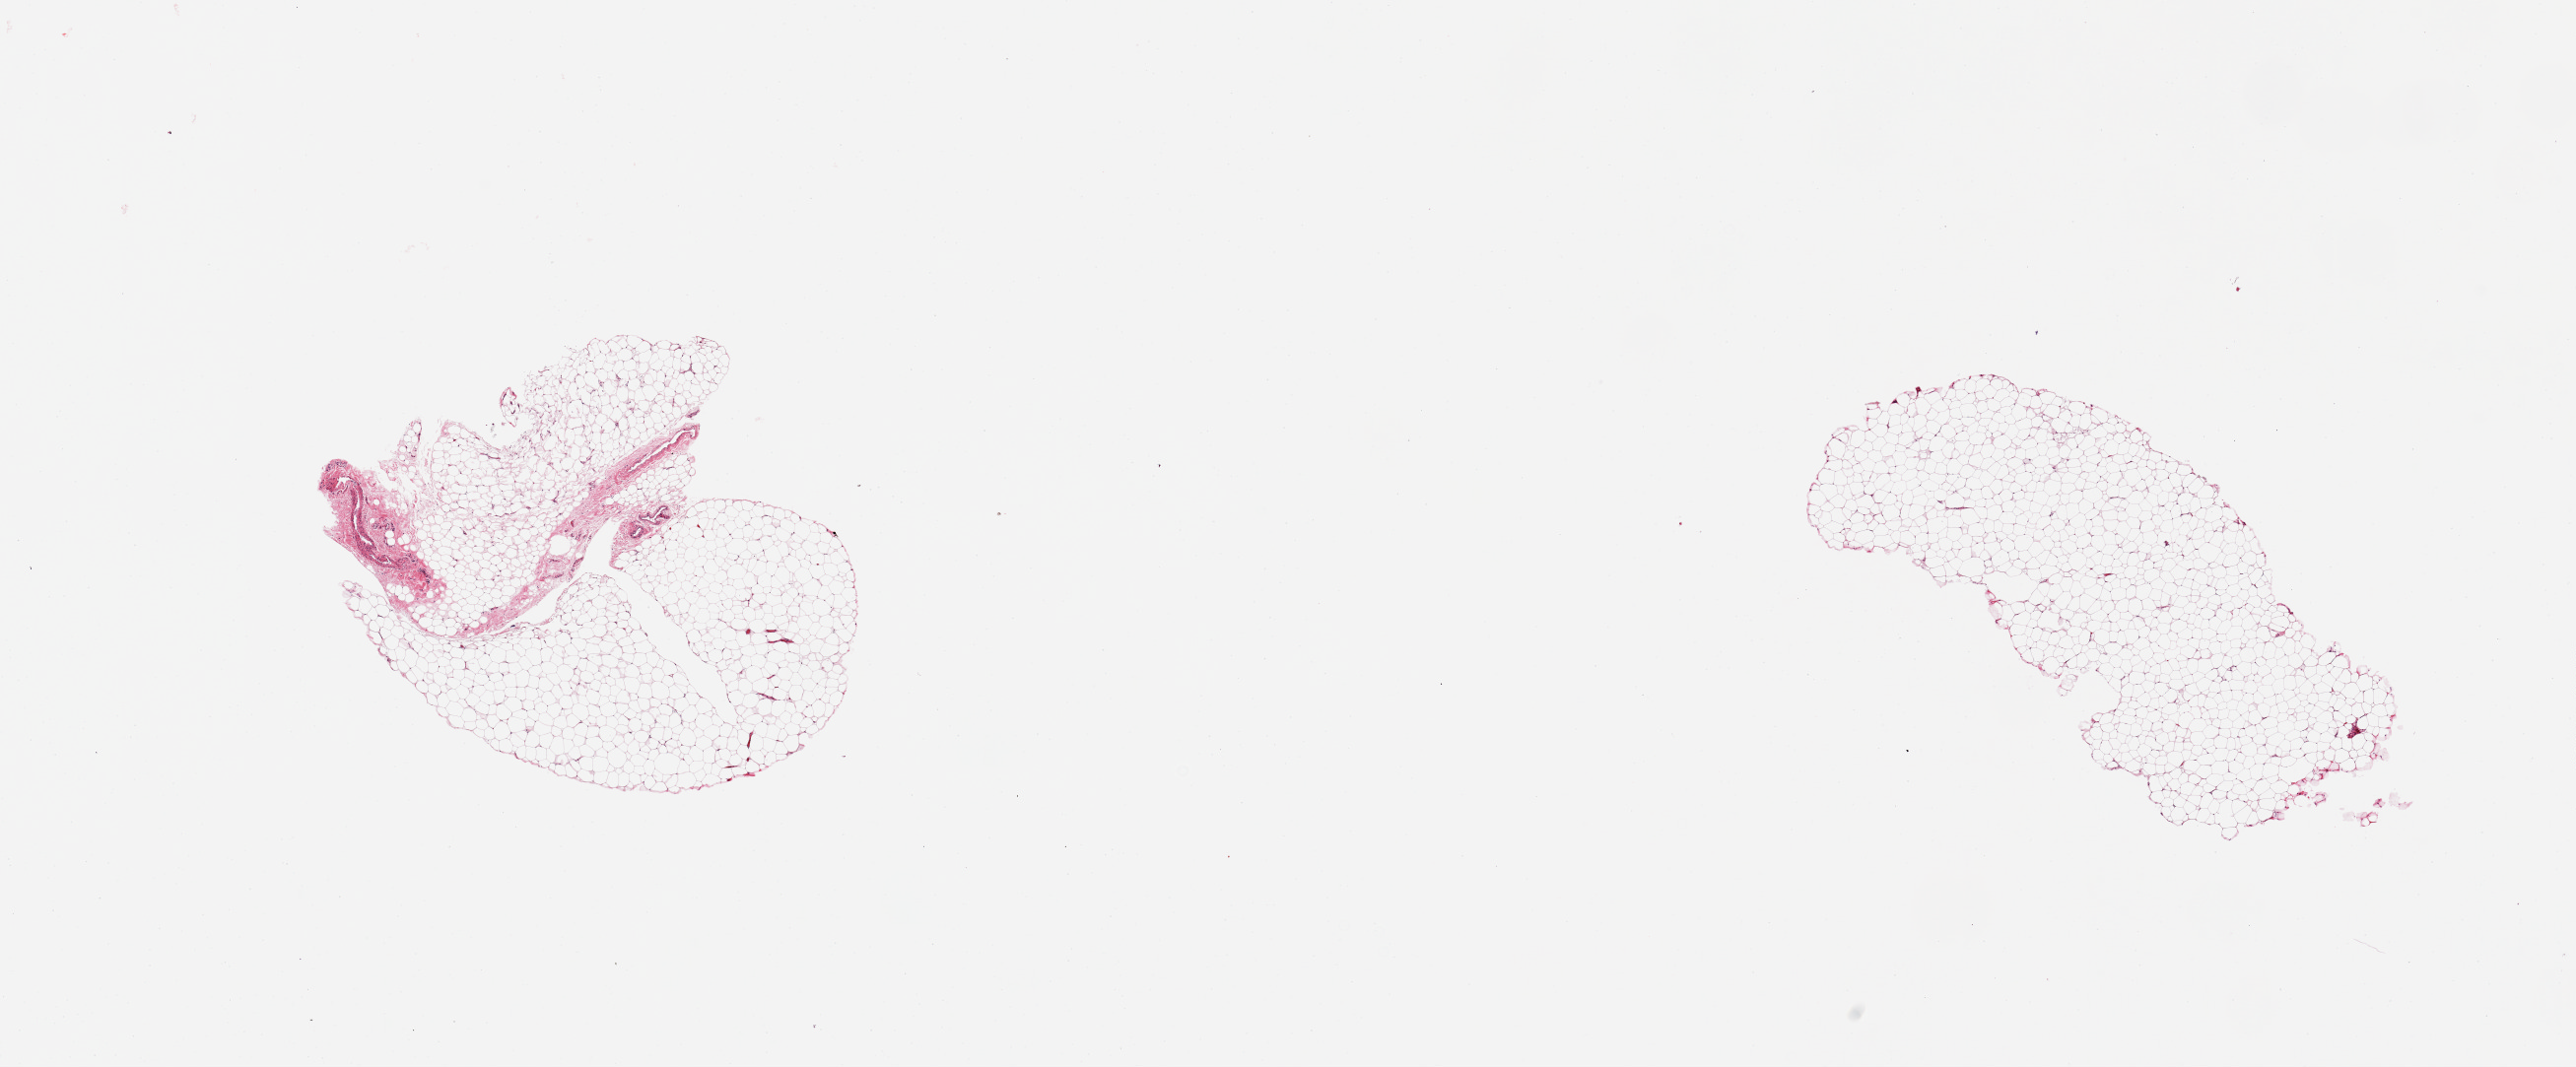
Digitized H&E-stained section, brightfield — a low-resolution overview of the entire scanned area, about 20.7 x 8.6 mm (from a 20x scan); PAXgene-fixed, paraffin-embedded tissue; sampled site (target tissue): adipose tissue; donor tissue sample. Donor sex: female.
Review note (as recorded): 2 pieces; ~5% of fibrovascular component on one piece.